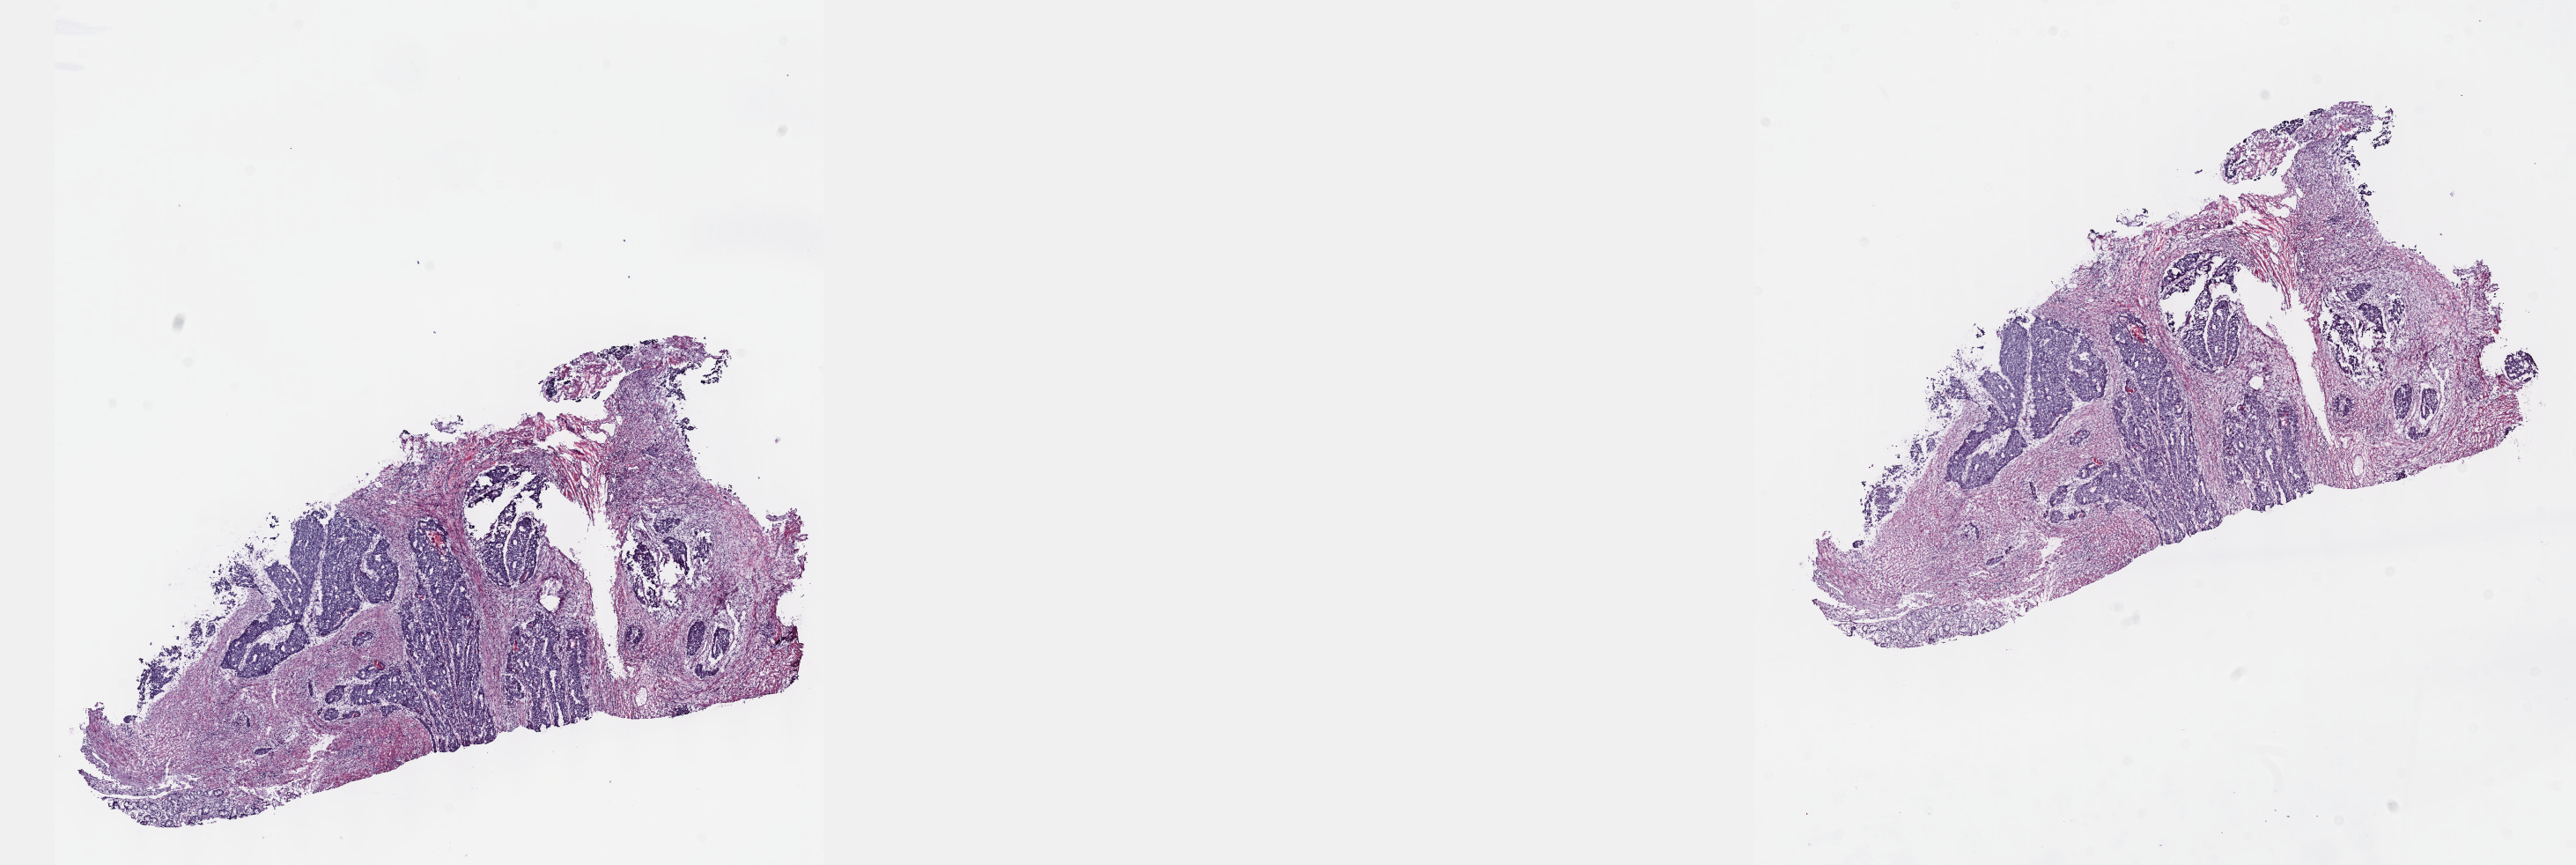
H&E whole-slide image — whole scanned area (about 23.6 x 7.9 mm, slide scanned at 40x) shown as a low-resolution overview. Frozen section. Stomach, primary tumour sample. Patient: male, age at initial diagnosis 57 years. Histologic grade: G2 (moderately differentiated). Pathologist review of this section (percent, as recorded): tumour cells 100%, tumour nuclei 60%, normal cells 0%, stromal cells 0%, necrosis 0%. Inflammatory infiltration, as recorded: lymphocyte infiltration 10%, monocyte infiltration 0%, neutrophil infiltration 0%.
- lymph nodes positive (case pathology): 8 of 29 examined
- pathologic diagnosis: Tubular adenocarcinoma (body of stomach)
- AJCC pathologic stage: IIIB (6th edition)